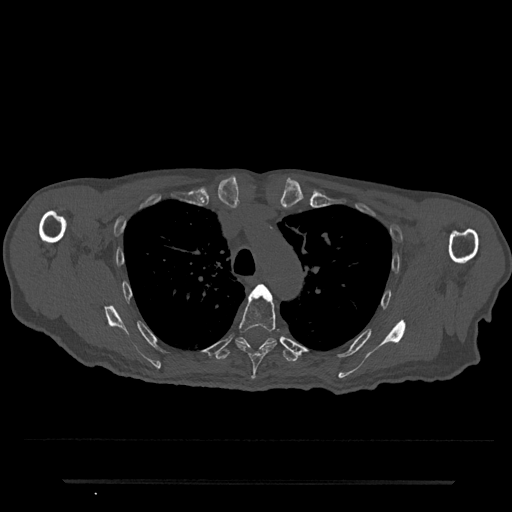
CT including the spine, one axial slice. Slice 567 of 797 in the series (ordered by position). Bone window (W 1800 / L 400 HU). 0.5 mm slice thickness. 512 × 512 image matrix, field of view 427 × 427 mm. Male patient, age 74 years. From the clinical record (not read from this slice): primary cancer: prostate.
Annotated regions visible in this slice (semi-automatic segmentation, software-assisted and operator-edited):
- T4 vertebra: box from (x=257, y=285) to (x=260, y=288) px
- T5 vertebra: (x=236, y=284)–(x=280, y=380)
- T6 vertebra: (x=215, y=337)–(x=299, y=362)